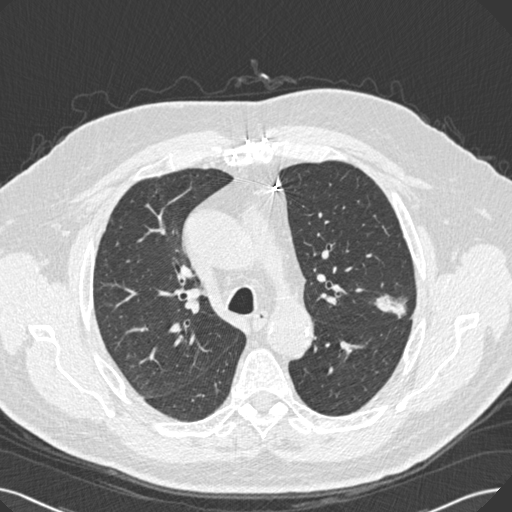
Low-dose screening chest CT, one axial slice; position 179 of 269 along the scan axis; reconstruction kernel B30f; lung window (W 1500 / L -600 HU); 1 mm slice thickness; 512 × 512 image matrix, field of view 370 × 370 mm.
Structures marked on this image (expert manual segmentation):
- lesion 1 (tumor, upper lobe of left lung): box from (x=374, y=294) to (x=407, y=319) px